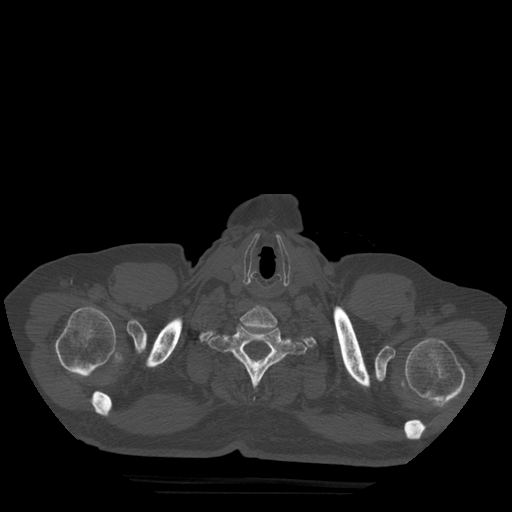
CT including the spine, one axial slice; bone window (W 1800 / L 400 HU); 1.25 mm slice thickness; 512 × 512 image matrix, field of view 420 × 420 mm. Patient age 72 years. From the clinical record (not read from this slice): primary cancer: prostate.
Structures marked on this image (semi-automatic segmentation, software-assisted and operator-edited):
- T1 vertebra: bounding box <208,324,307,387> (left, top, right, bottom; pixels)